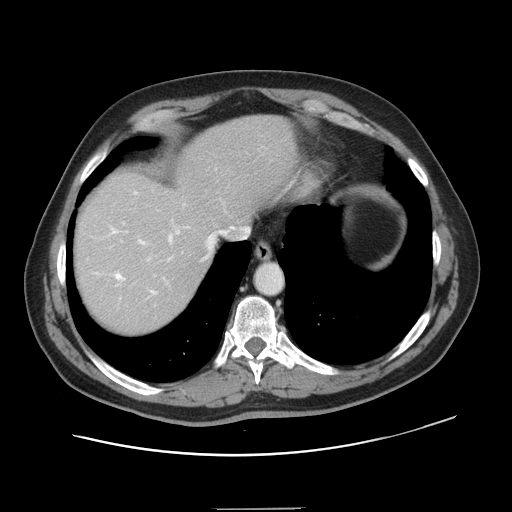
Contrast-enhanced abdominal CT, one axial slice. Slice 123 of 143 in the series (ordered by position). 120 kVp. Intravenous contrast given. Soft-tissue window (W 400 / L 40 HU). 2.5 mm slice thickness. 512 × 512 image matrix. Male patient, age 62 years. From the clinical record (not read from this slice): diagnosis: colorectal cancer liver metastases, imaged before liver resection; multiple liver metastases: yes; largest metastasis: 2.7 cm; chemotherapy before resection: yes.
Structures marked on this image (manually delineated by an expert):
- hepatic veins: bounding box (x1, y1, x2, y2) in pixels: (112, 192, 213, 294)
- liver: (75, 115, 296, 335)
- planned liver remnant (the part of the liver to remain after resection): (75, 115, 295, 294)
- portal vein (with intrahepatic branches): (121, 223, 186, 261)